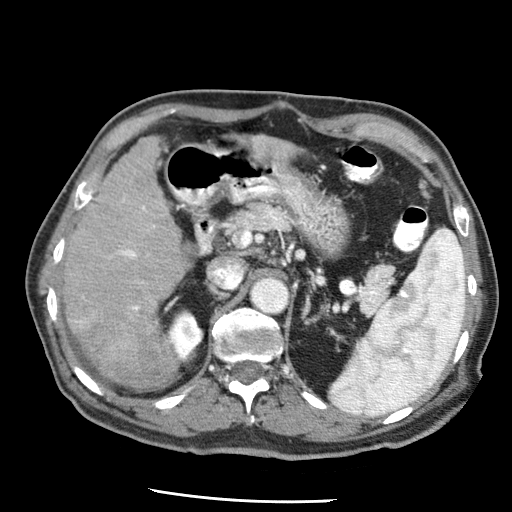
Contrast-enhanced abdominal CT (liver protocol), one axial slice. Position 27 of 79 along the scan axis. Reconstruction kernel STANDARD. 120 kVp. Soft-tissue window (W 400 / L 40 HU). 2.5 mm slice thickness. 512 × 512 image matrix, field of view 320 × 320 mm. From the clinical record (not read from this slice): diagnosis: hepatocellular carcinoma (patient treated with transarterial chemoembolisation; whether this scan precedes or follows treatment is not stated here); TNM stage (as recorded): Stage-IIIA; Child-Pugh class: A; tumour nodularity: multinodular; tumour size: 7 cm.
Annotated regions visible in this slice (semi-automatic segmentation, software-assisted and operator-edited):
- liver parenchyma outside the tumour (the mass and vessels are separate outlines, so this box may not span the whole liver): bounding box (x1, y1, x2, y2) in pixels: (60, 136, 188, 378)
- liver vessels: (76, 199, 155, 323)